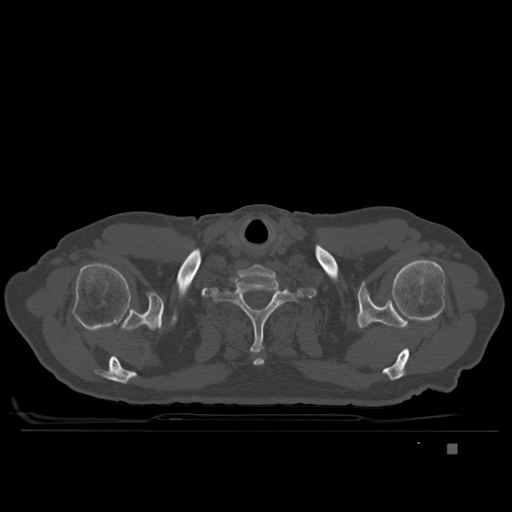
CT including the spine, one axial slice; slice 325 of 435 in the series (ordered by position); bone window (W 1800 / L 400 HU); 1.5 mm slice thickness; 512 × 512 image matrix. Patient: male, 73 years. Case-level facts recorded for this patient, not image findings: primary cancer: skin.
Structures marked on this image (semi-automatic segmentation, software-assisted and operator-edited):
- T1 vertebra: box from (x=212, y=274) to (x=301, y=354) px